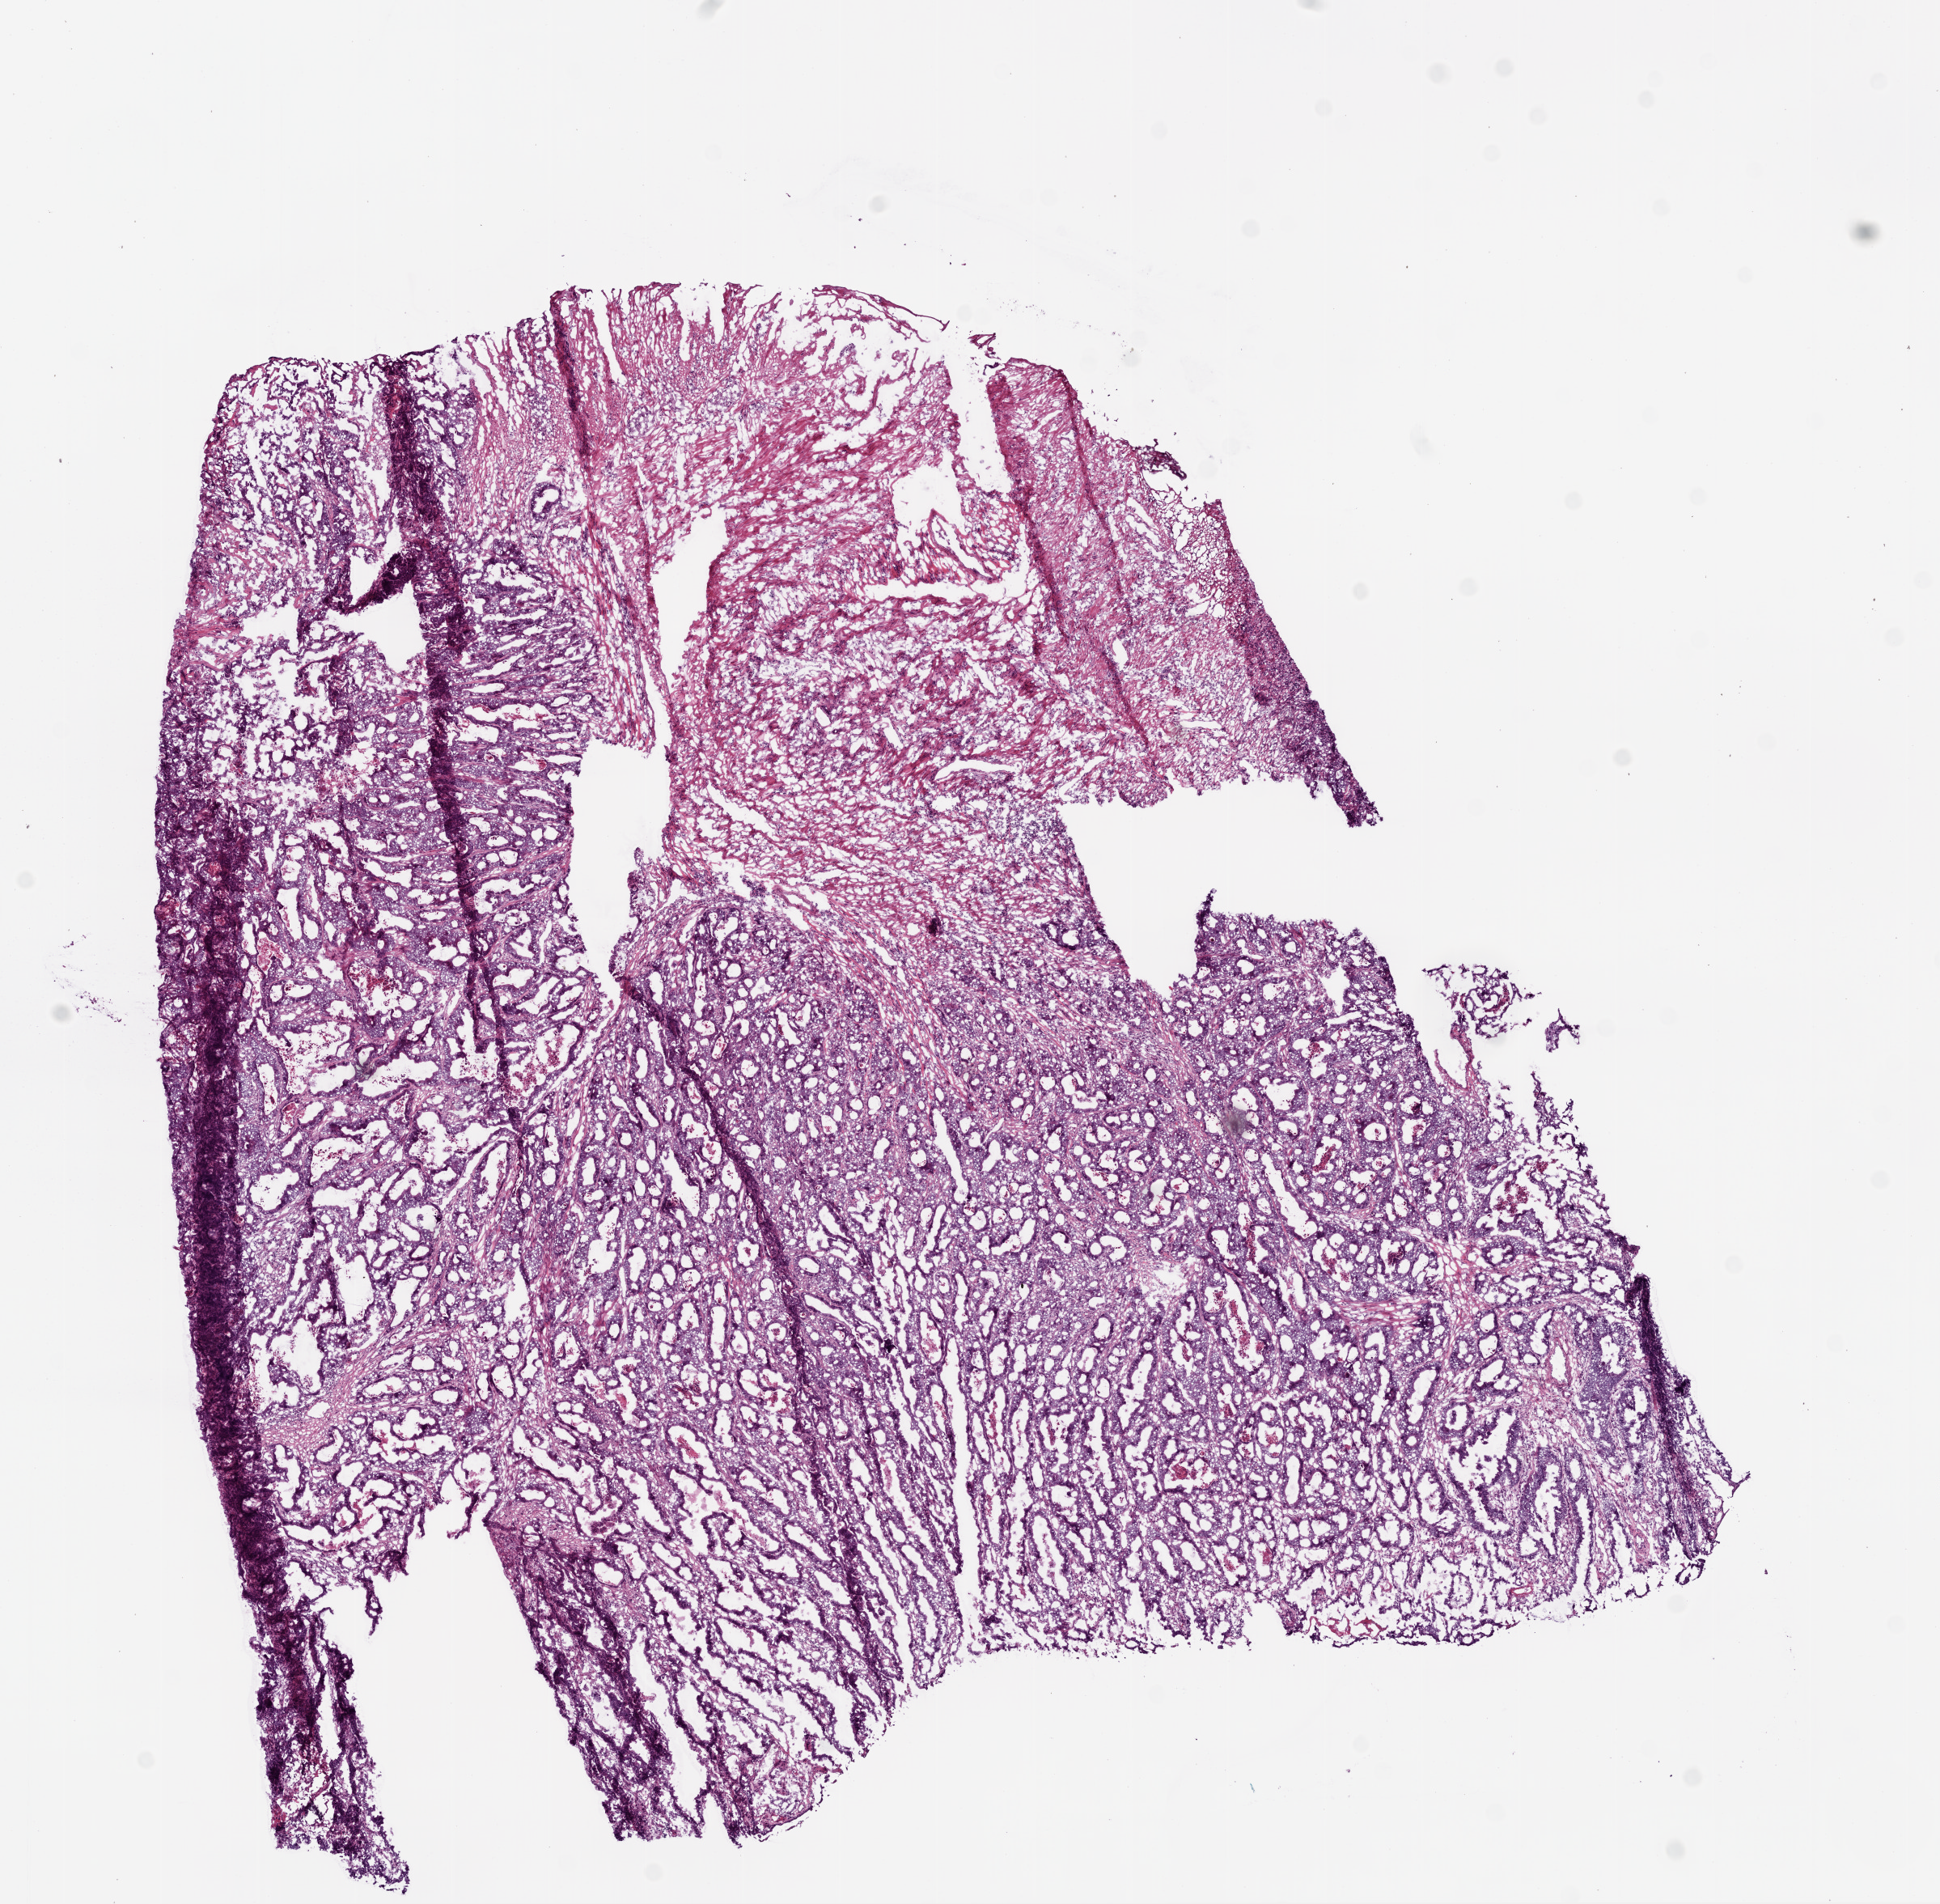
Digitized H&E tissue section (whole slide), whole scanned area (about 9.7 x 9.5 mm, from a 20x scan) shown as a low-resolution overview; frozen section from the bottom of the tissue portion; rectum, primary tumour sample. Patient: male, age at initial diagnosis 72 years. Slide review estimates, as recorded: tumour cells 74%, tumour nuclei 80%, normal cells 0%, stromal cells 18%, necrosis 8%.
AJCC pathologic stage: IIA (7th edition). TNM: T3 N0 M0. Histologic diagnosis: Adenocarcinoma, NOS.